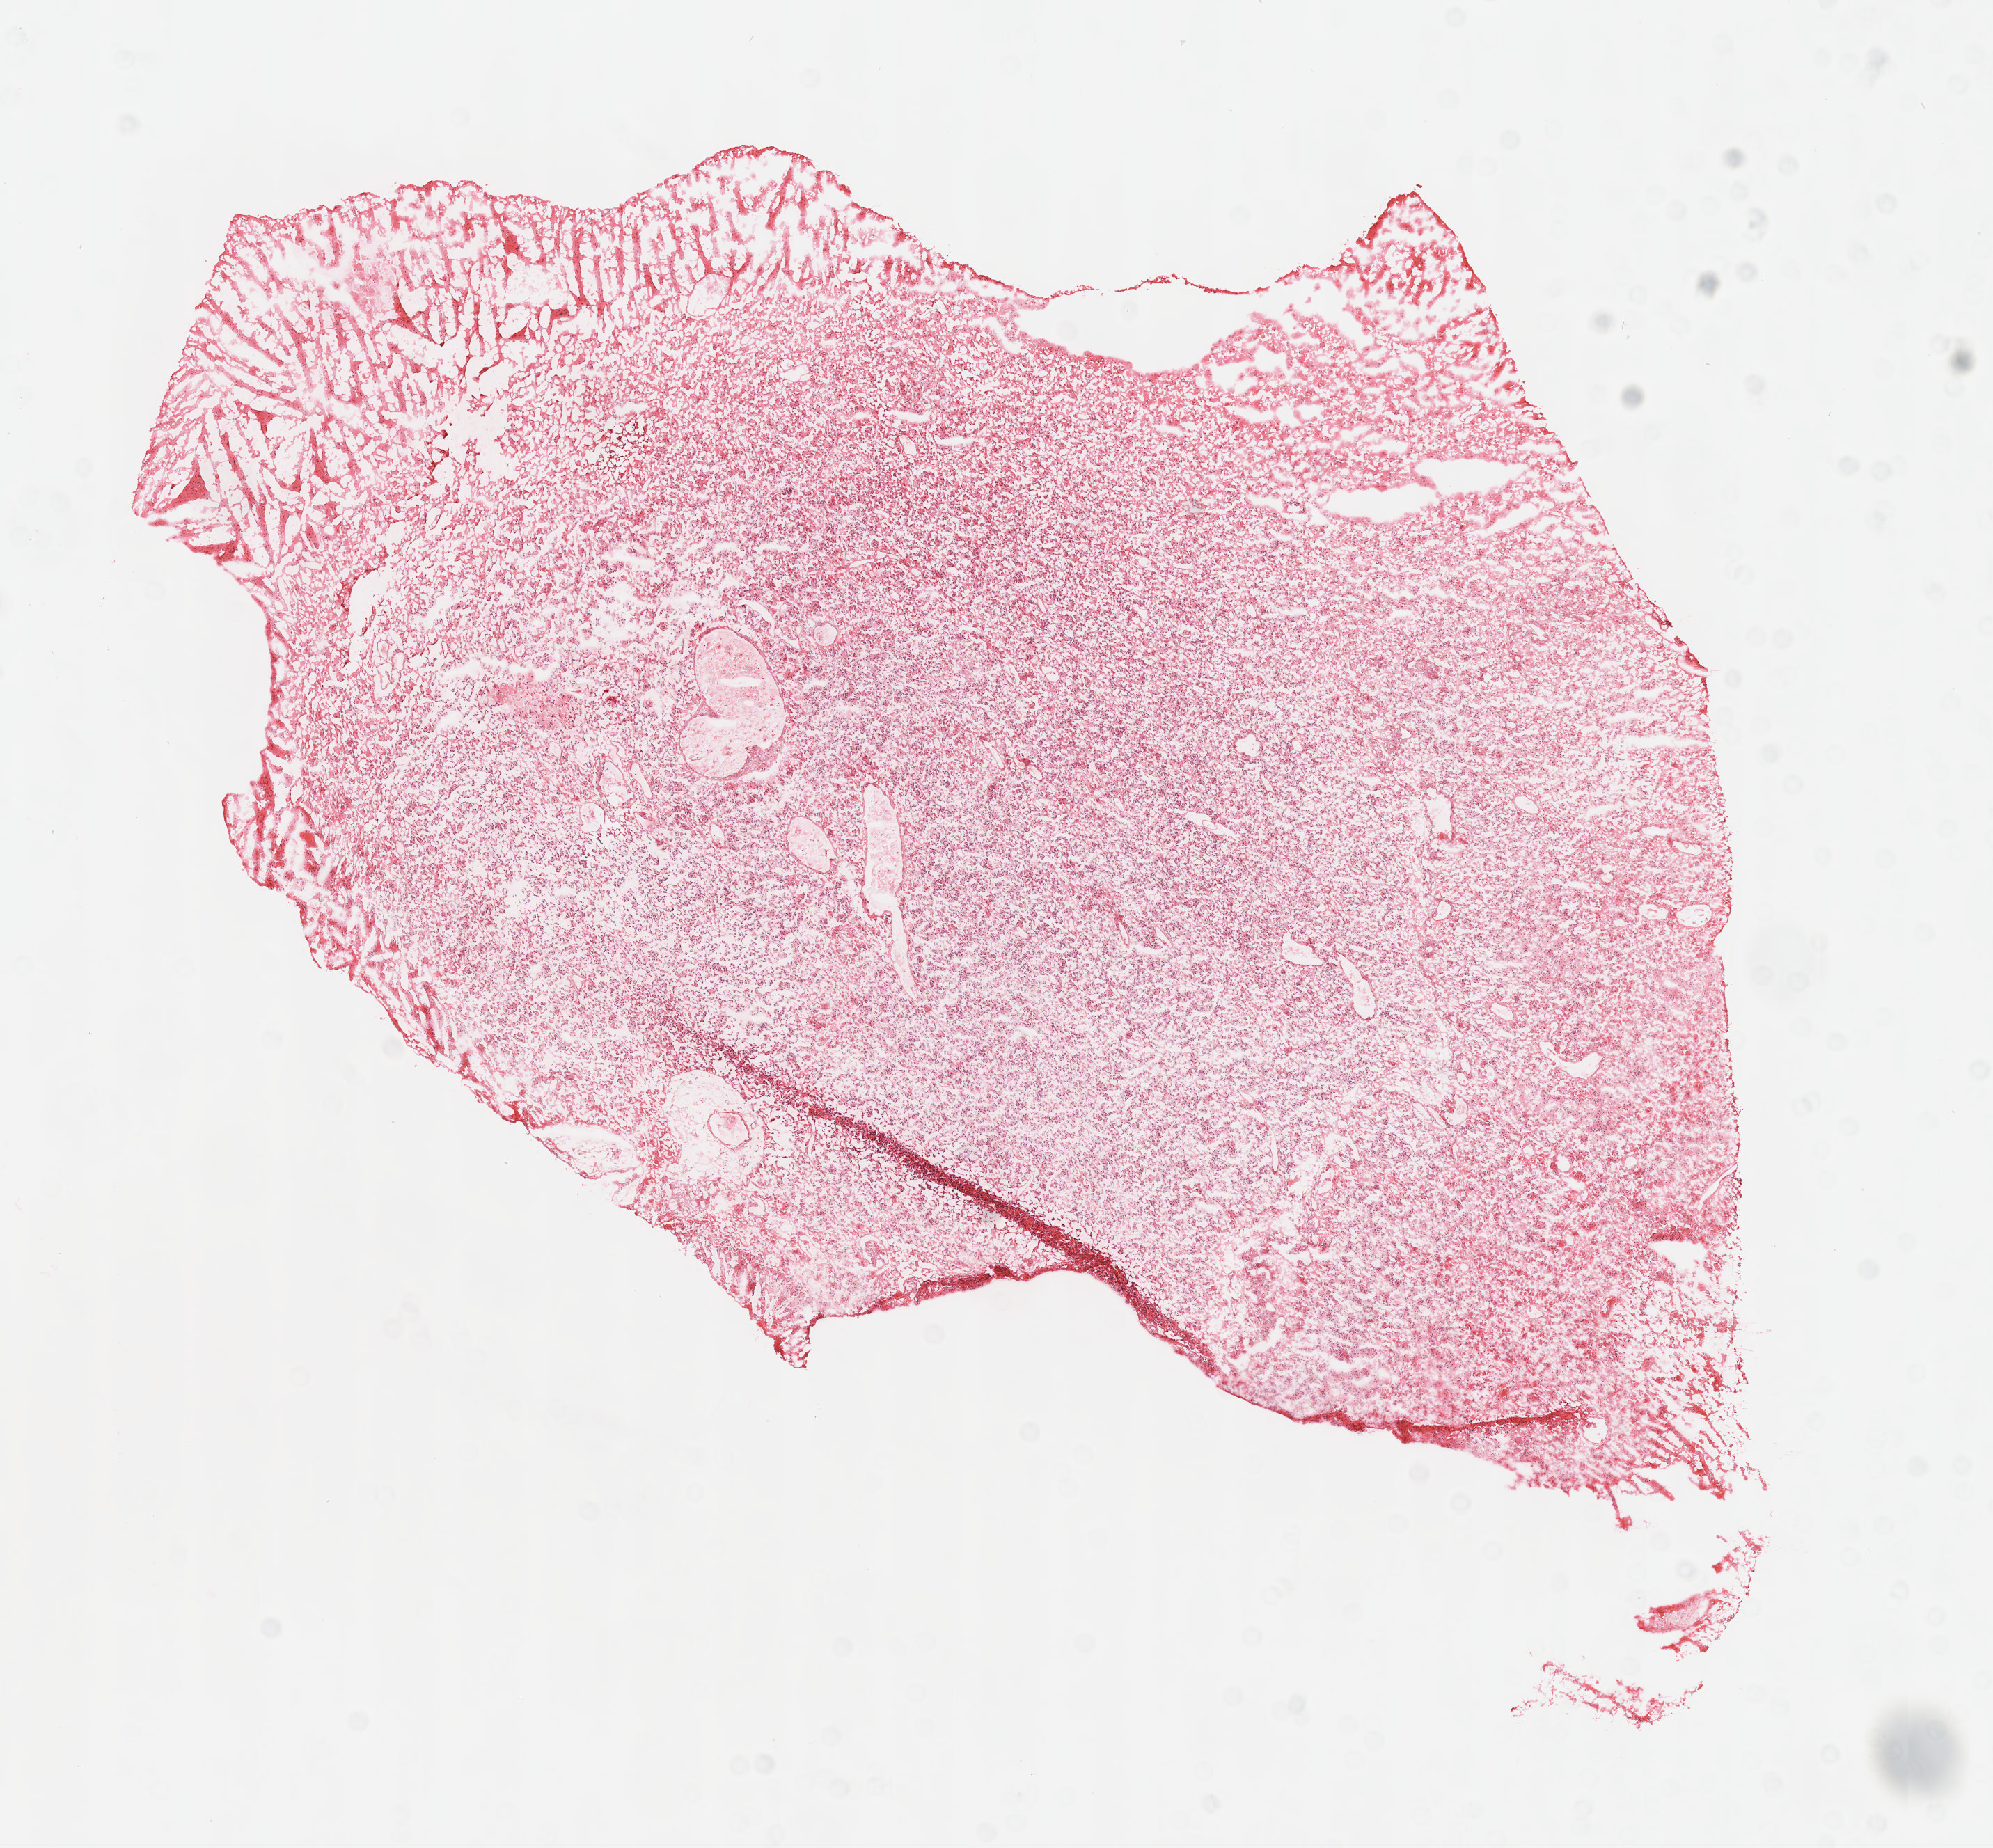
H&E-stained whole-slide image, whole scanned area (about 11.6 x 10.7 mm) shown as a low-resolution overview; frozen section from the top of the tissue portion; brain, primary tumour sample. Male patient; age at initial diagnosis 62 years. Composition of this section per pathologist review: tumour cells 100%, tumour nuclei 100%, normal cells 0%, stromal cells 0%, necrosis 0%. Inflammatory infiltration, as recorded: lymphocyte infiltration 0%.
Diagnosis: Glioblastoma.